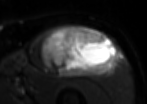
MRI of an extremity soft-tissue mass, one axial slice; position 56 of 85 along the scan axis; T2-weighted fat-saturated; MR volume resampled by the dataset authors to the PET/CT grid (not the native acquisition matrix); 3.27 mm slice thickness; 147 × 104 image matrix, field of view 144 × 102 mm. Male patient. Case-level facts recorded for this patient, not image findings: histological type: extraskeletal osteosarcoma; grade: high; site of the primary tumour: thigh.
Annotated regions visible in this slice (expert contour drawn on MRI and transferred to this co-registered scan by the dataset authors):
- gross tumour volume (mass): bounding box [x1, y1, x2, y2] px = [40, 24, 121, 77]